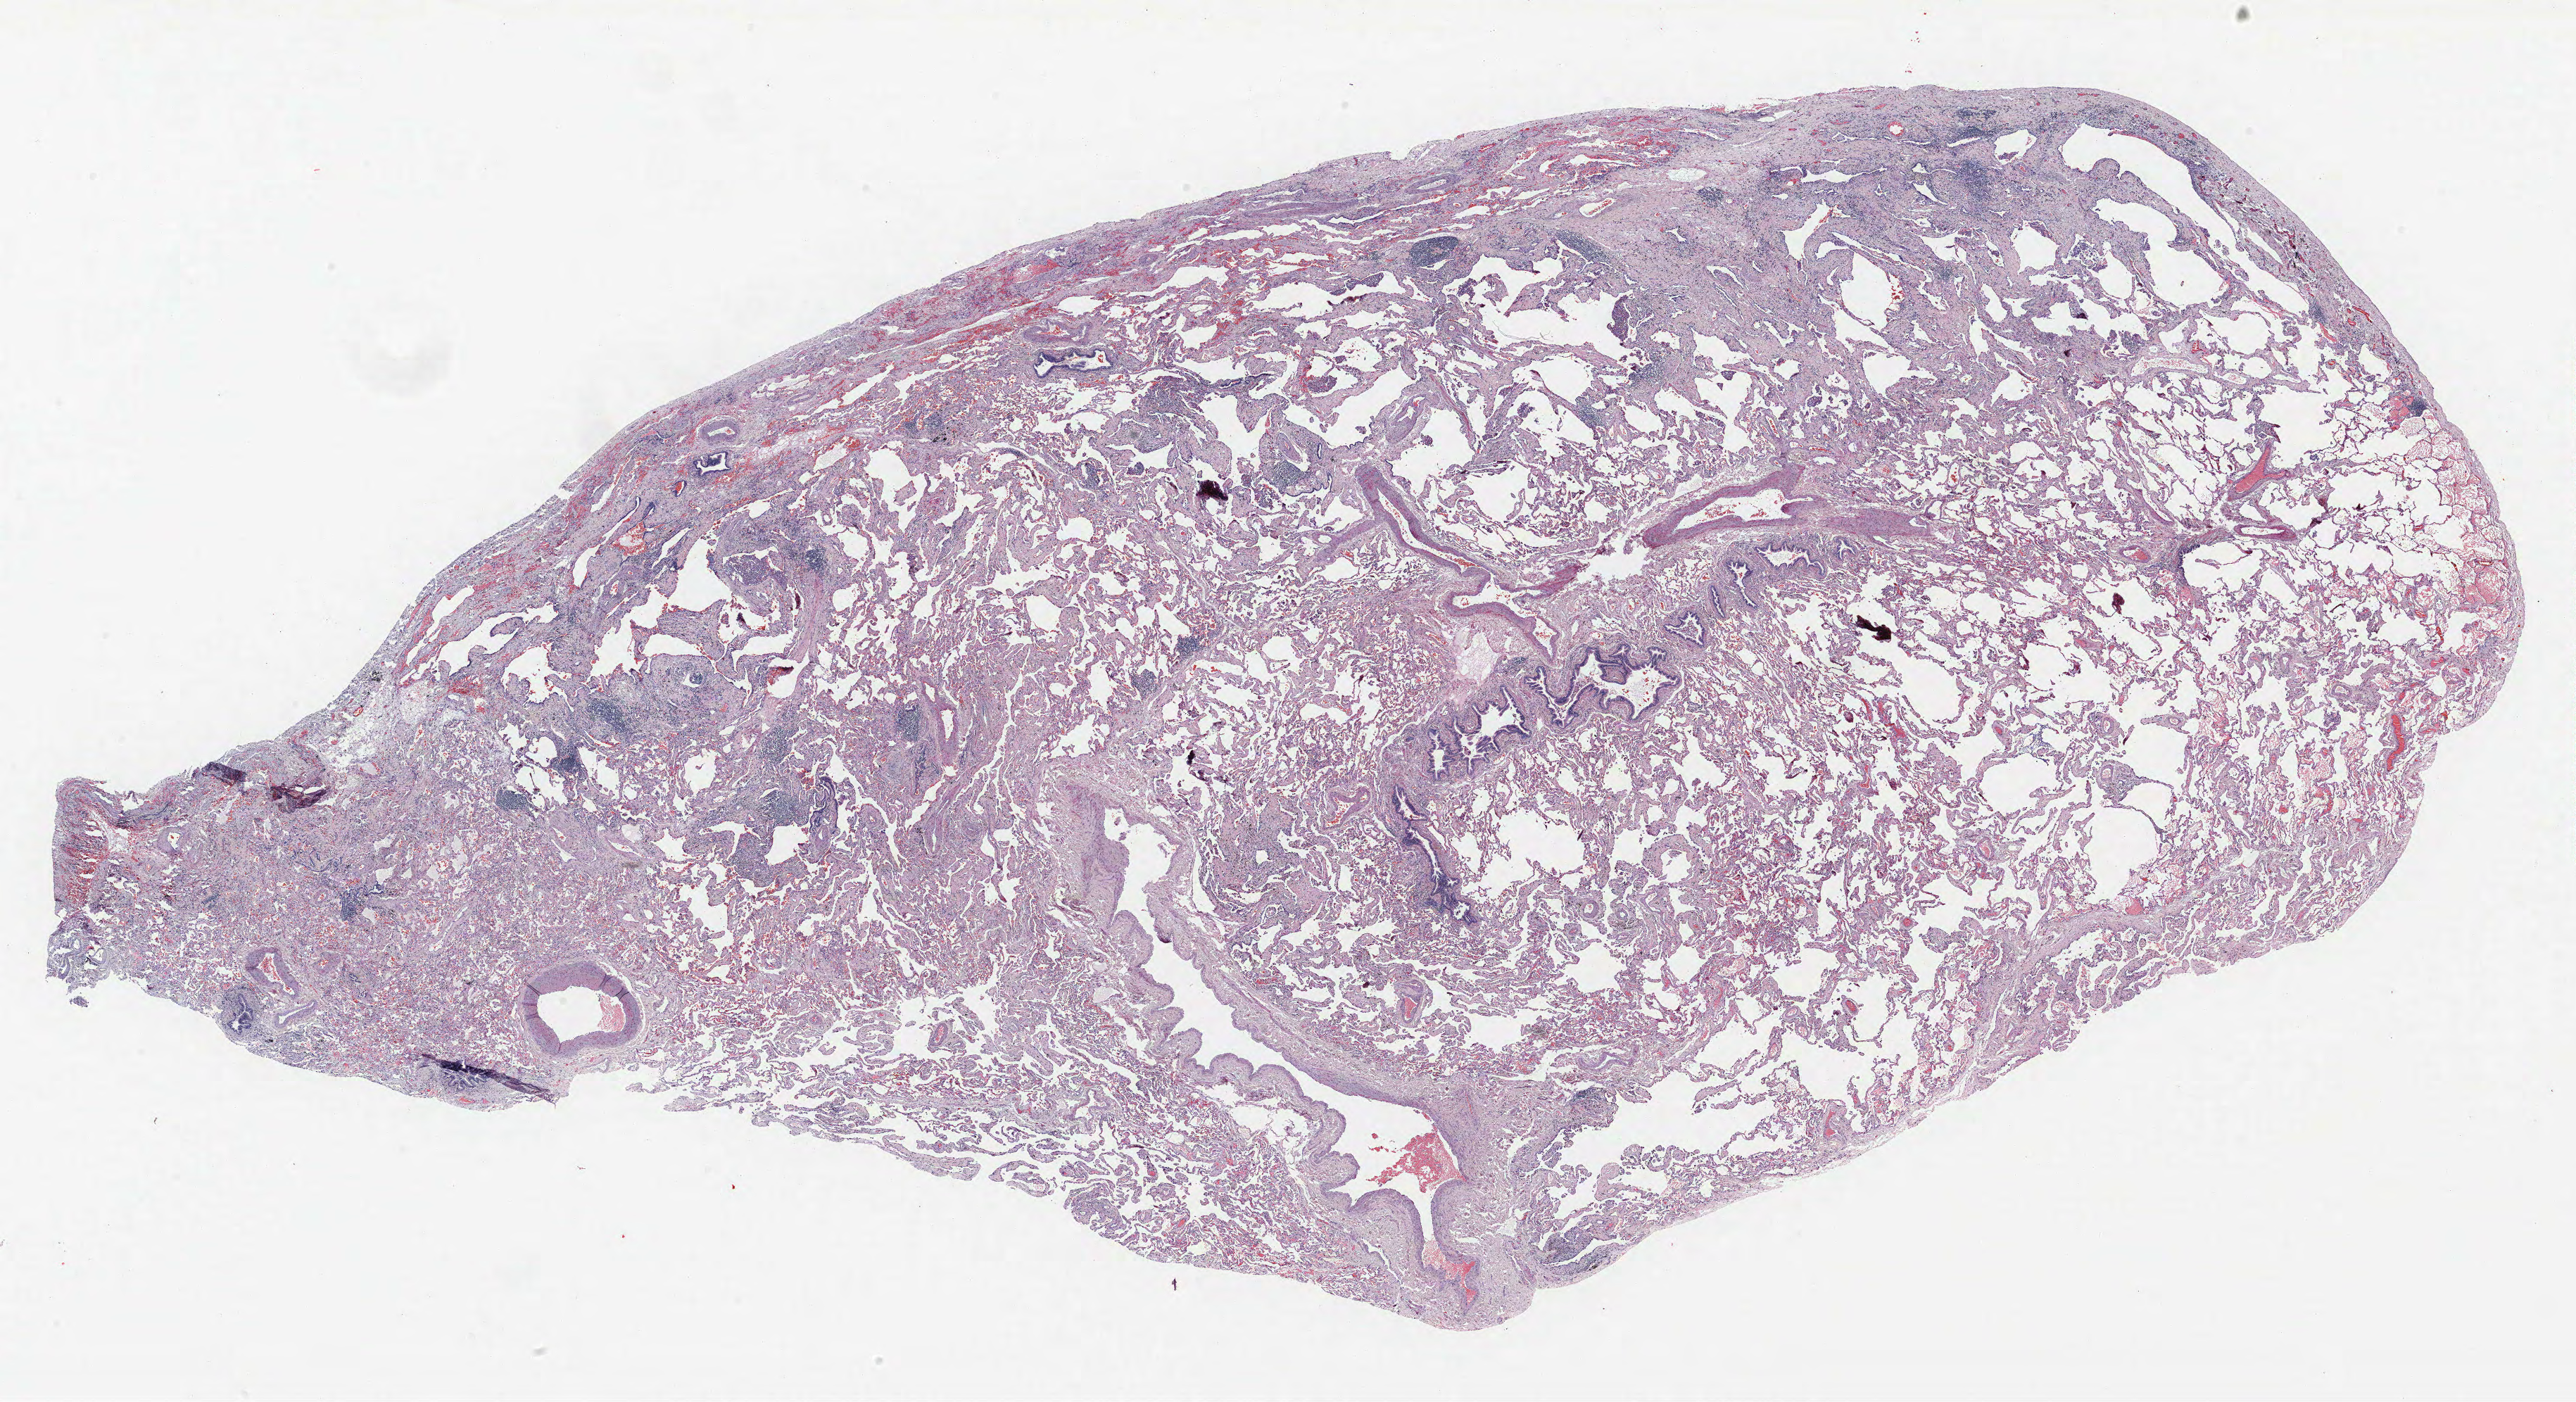
Hematoxylin and eosin (H&E) stained whole-slide image — low-resolution overview of the scanned area, about 29.3 x 15.9 mm (slide scanned at 40x). Formalin-fixed paraffin-embedded (FFPE) section. Lung tissue. Male patient, aged 68 at enrolment. Former smoker at enrolment. Grade: moderately differentiated (G2).
• primary tumour location (clinical record): left upper lobe
• participant's lung-cancer diagnosis: Squamous cell carcinoma, NOS (ICD-O-3 8070/3)
• tumour size (pathology): 17 mm
• stage (AJCC 6th edition): IA